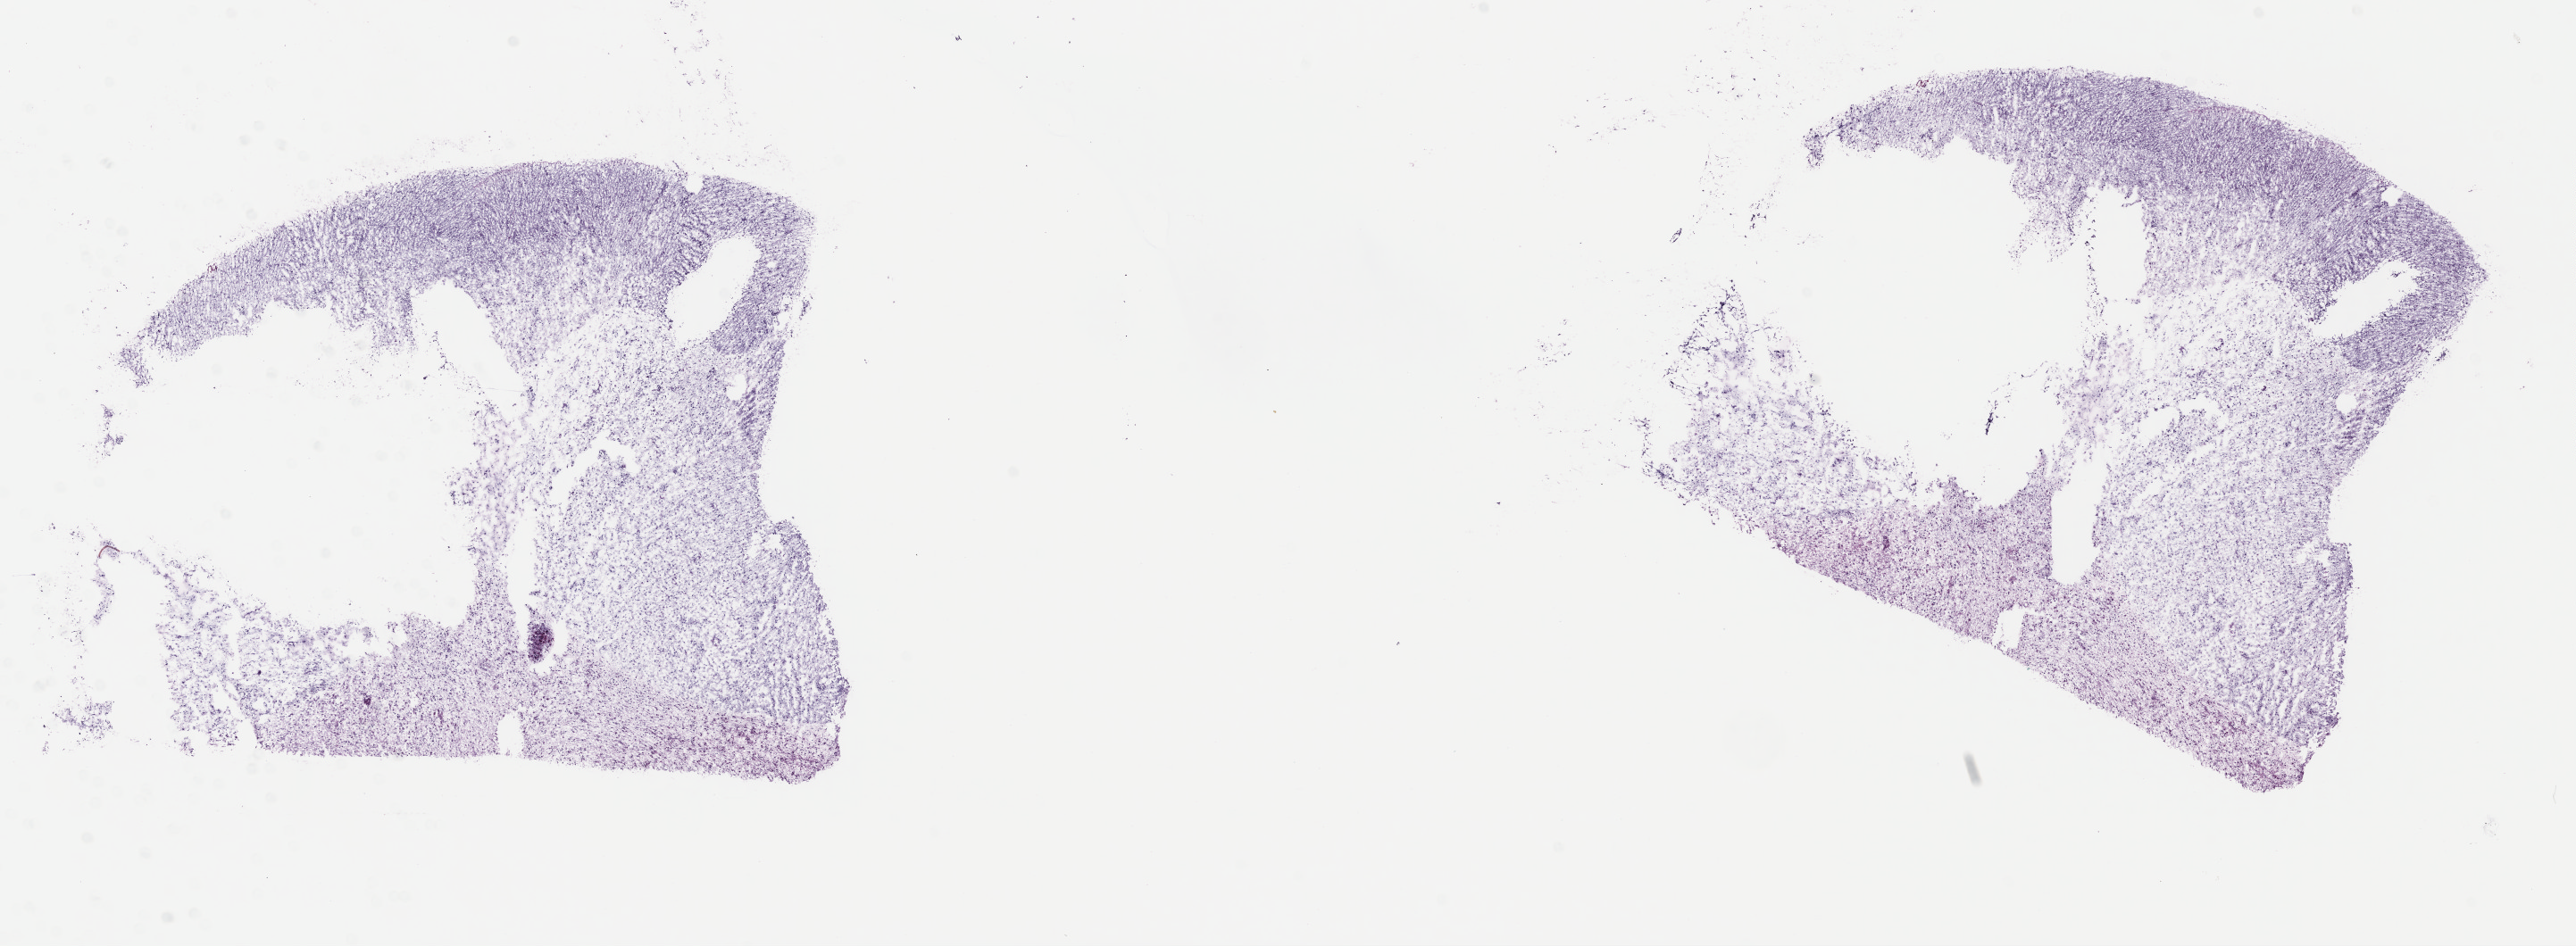
Digitized H&E tissue section (whole slide), a low-resolution overview of the entire scanned area, about 22.7 x 8.3 mm; frozen section from the top of the tissue portion; sample: recurrent tumour, brain. Female patient; age at initial diagnosis 35 years. Slide review estimates, as recorded: tumour cells 45%, tumour nuclei 70%, normal cells 10%, stromal cells 45%, necrosis 0%. Infiltration values recorded for this section: lymphocyte infiltration 0%, monocyte infiltration 0%, neutrophil infiltration 0%.
* this section: recurrent tumour
* patient diagnosis: Oligodendroglioma, NOS (cerebrum)